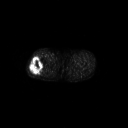
FDG PET of an extremity soft-tissue mass (from a PET/CT study), one axial slice; position 249 of 267 along the scan axis; 128 × 128 image matrix, field of view 700 × 700 mm. Patient: male, 43 years. From the clinical record (not read from this slice): histological type: poorly differentiated synovial sarcoma; grade: high; site of the primary tumour: right buttock.
Structures marked on this image (expert contour drawn on MRI and transferred to this co-registered scan by the dataset authors):
- gross tumour volume including surrounding oedema: bounding box [x1, y1, x2, y2] px = [29, 57, 44, 75]
- gross tumour volume (mass): [29, 57, 44, 75]